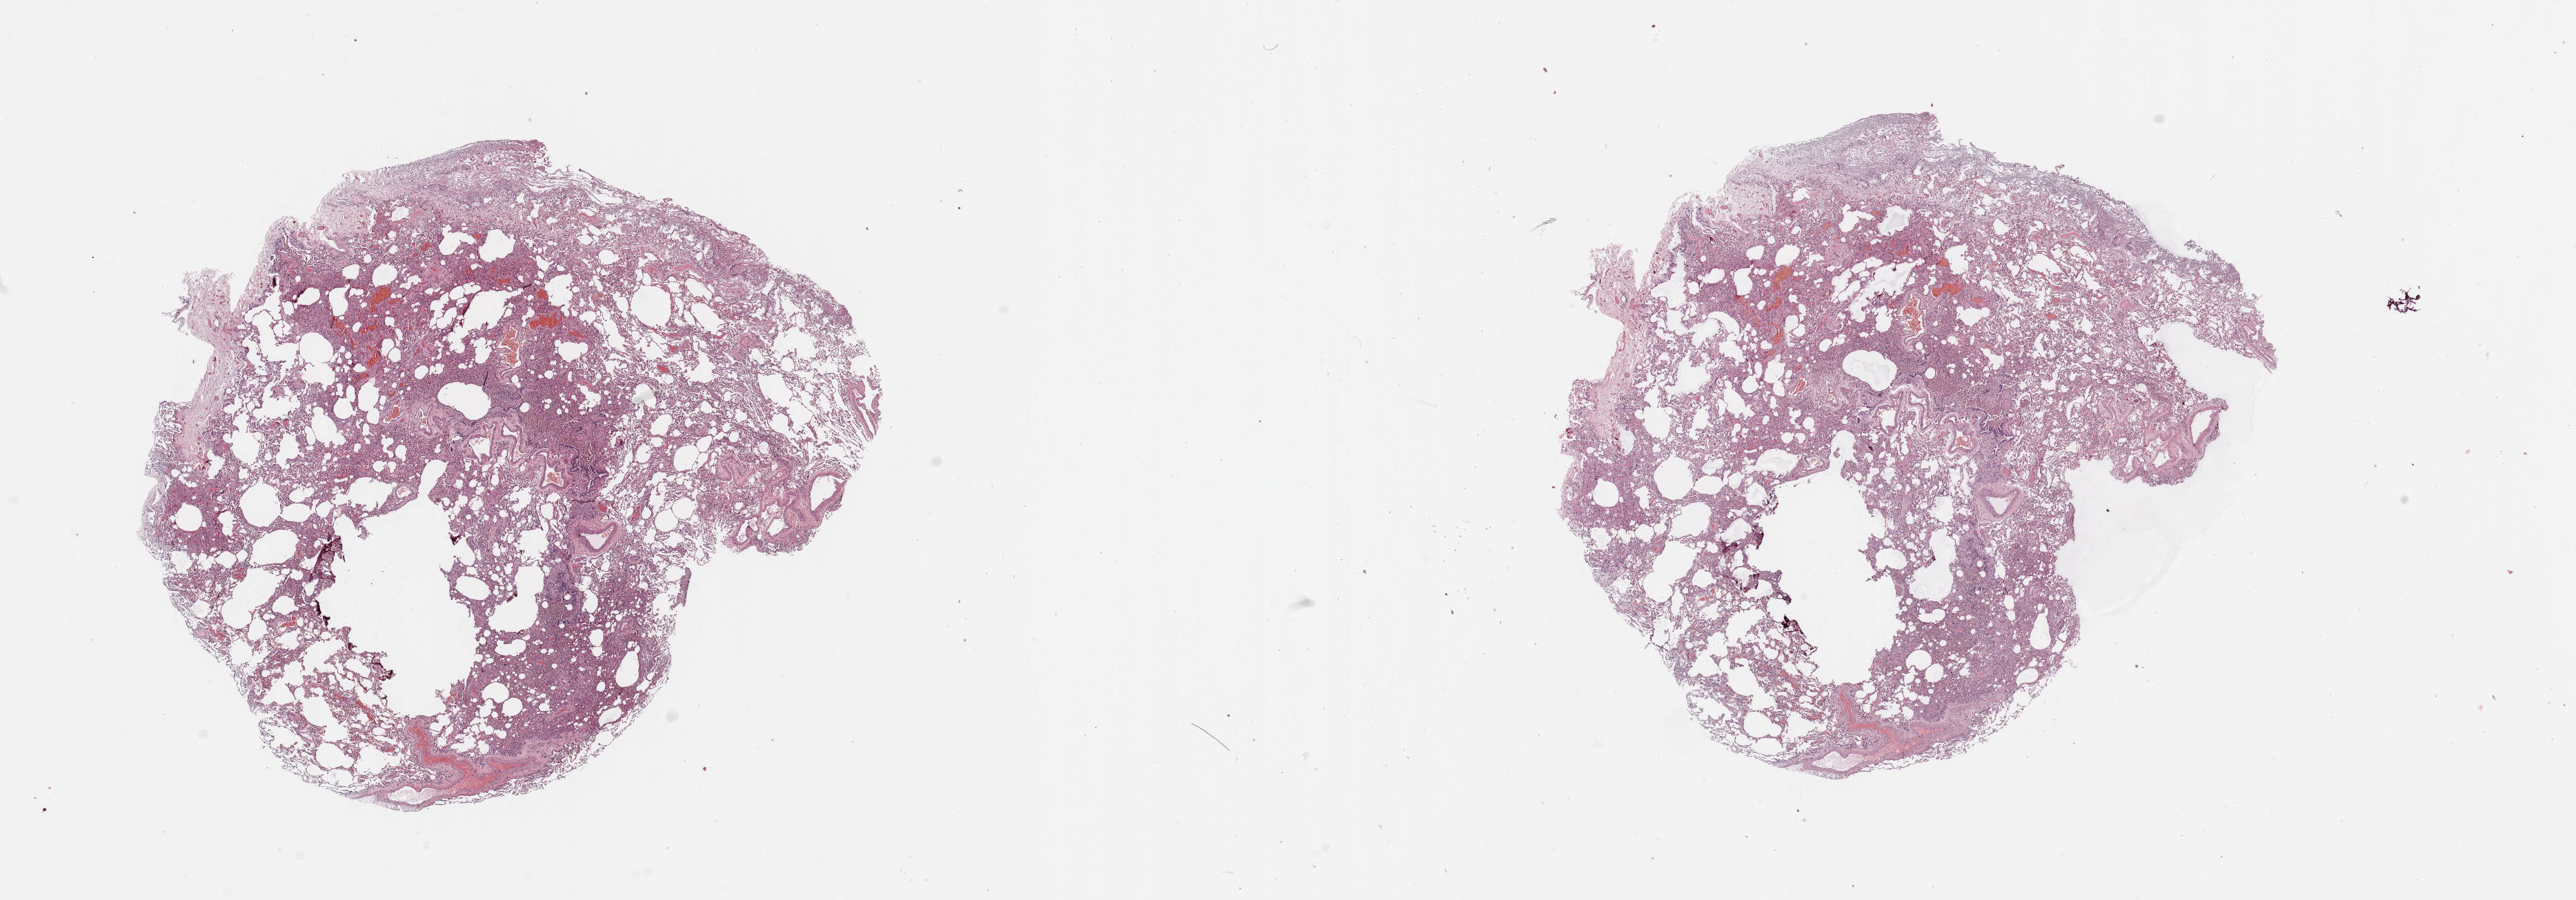
Whole-slide histology image, Hematoxylin and eosin (H&E) stained, whole scanned area (about 29.5 x 10.3 mm, slide scanned at 20x) shown as a low-resolution overview, lung, normal (non-tumour) tissue. Patient: male, age 57 years.
- this section: normal (non-tumour) tissue from the same patient
- patient diagnosis: Squamous cell carcinoma, NOS